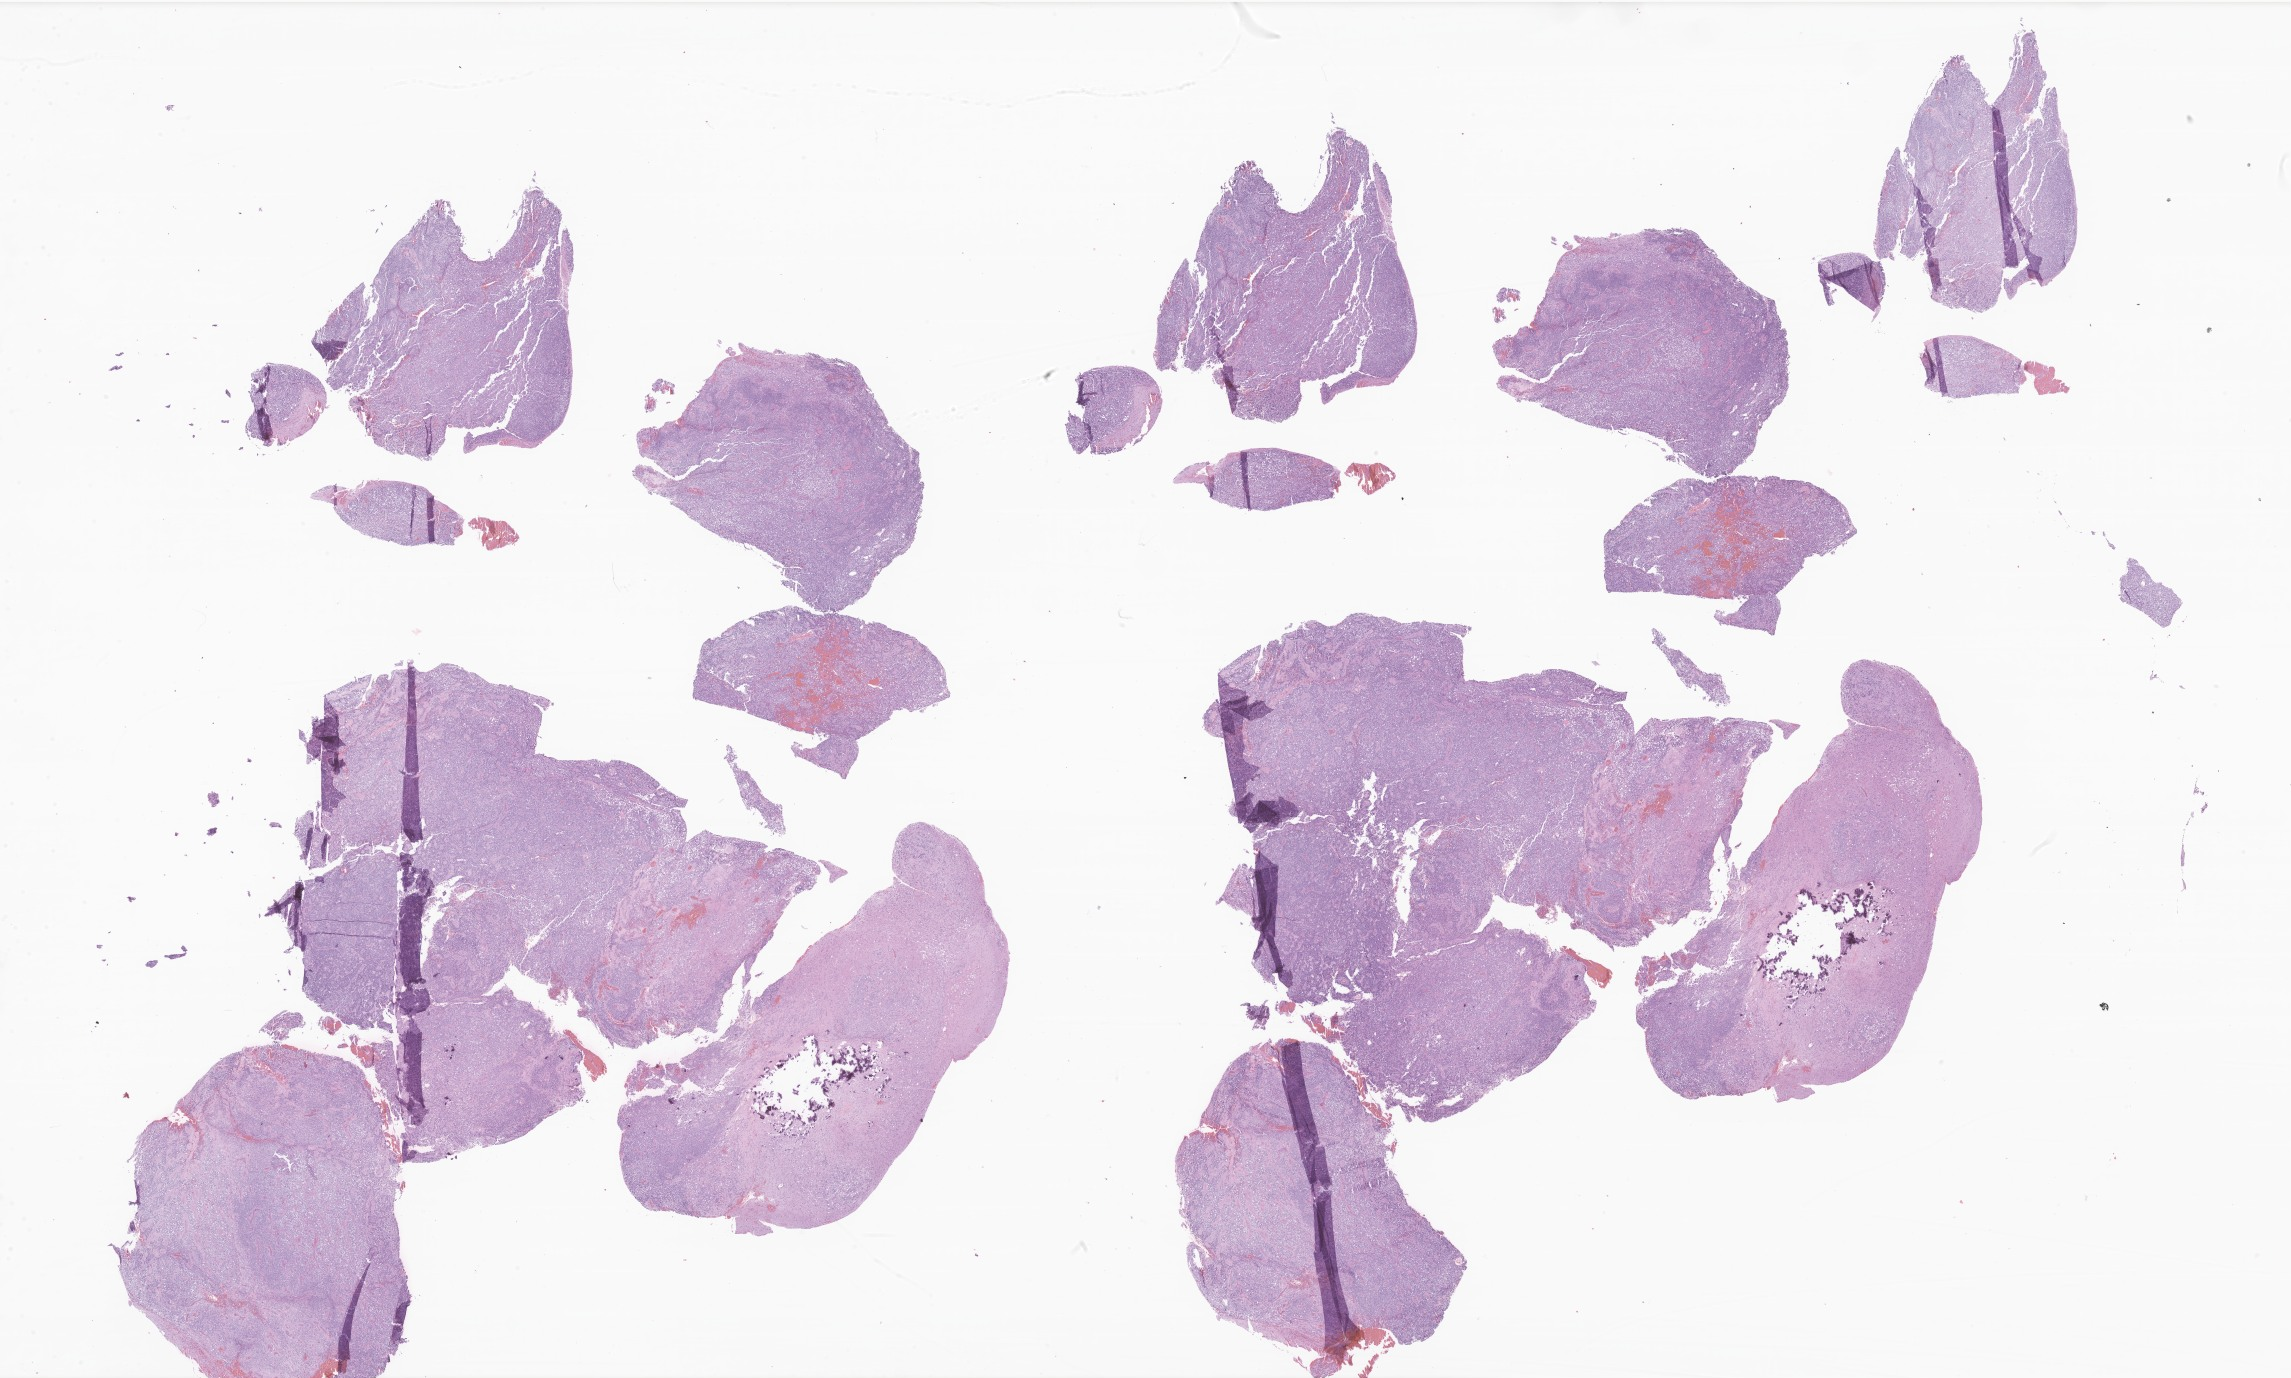
Digitized H&E-stained section of tumor tissue from the brain, a low-resolution overview of the entire scanned area, about 38.6 x 23.2 mm. Formalin-fixed paraffin-embedded section. Female patient, age 231 months (19 years 3 months).
* recorded diagnosis: Ependymoma, NOS